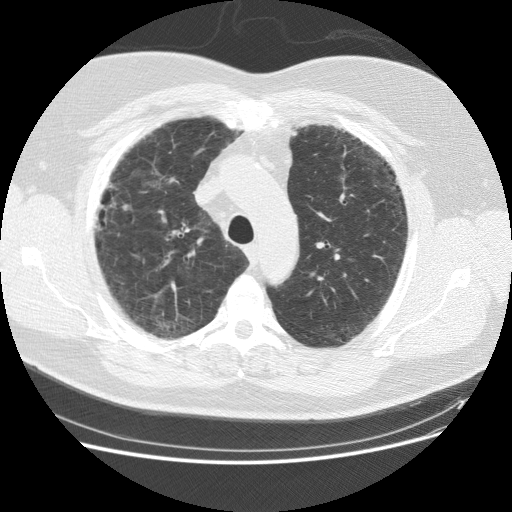
Chest CT (low-dose screening protocol), one axial image; first (baseline) screen; lung window (W 1500 / L -600 HU); 2.5 mm slice thickness; 120 kVp; slice 34 of 151 in the series. Male participant, aged 59 years at enrolment. Current smoker at enrolment.
• Expert-annotated lung lesion, bounding box [x1, y1, x2, y2] px = [84, 163, 139, 233].
• The screening reader recorded 2 non-calcified nodules or masses ≥4 mm on this exam (right middle lobe, right lower lobe); which of them this box marks is not recorded.
• Later outcome: lung cancer diagnosed 338 days after this screen — adenocarcinoma, NOS, right upper lobe, right middle lobe, moderately differentiated (G2), stage IA (AJCC 6th edition), 13 mm at pathology.